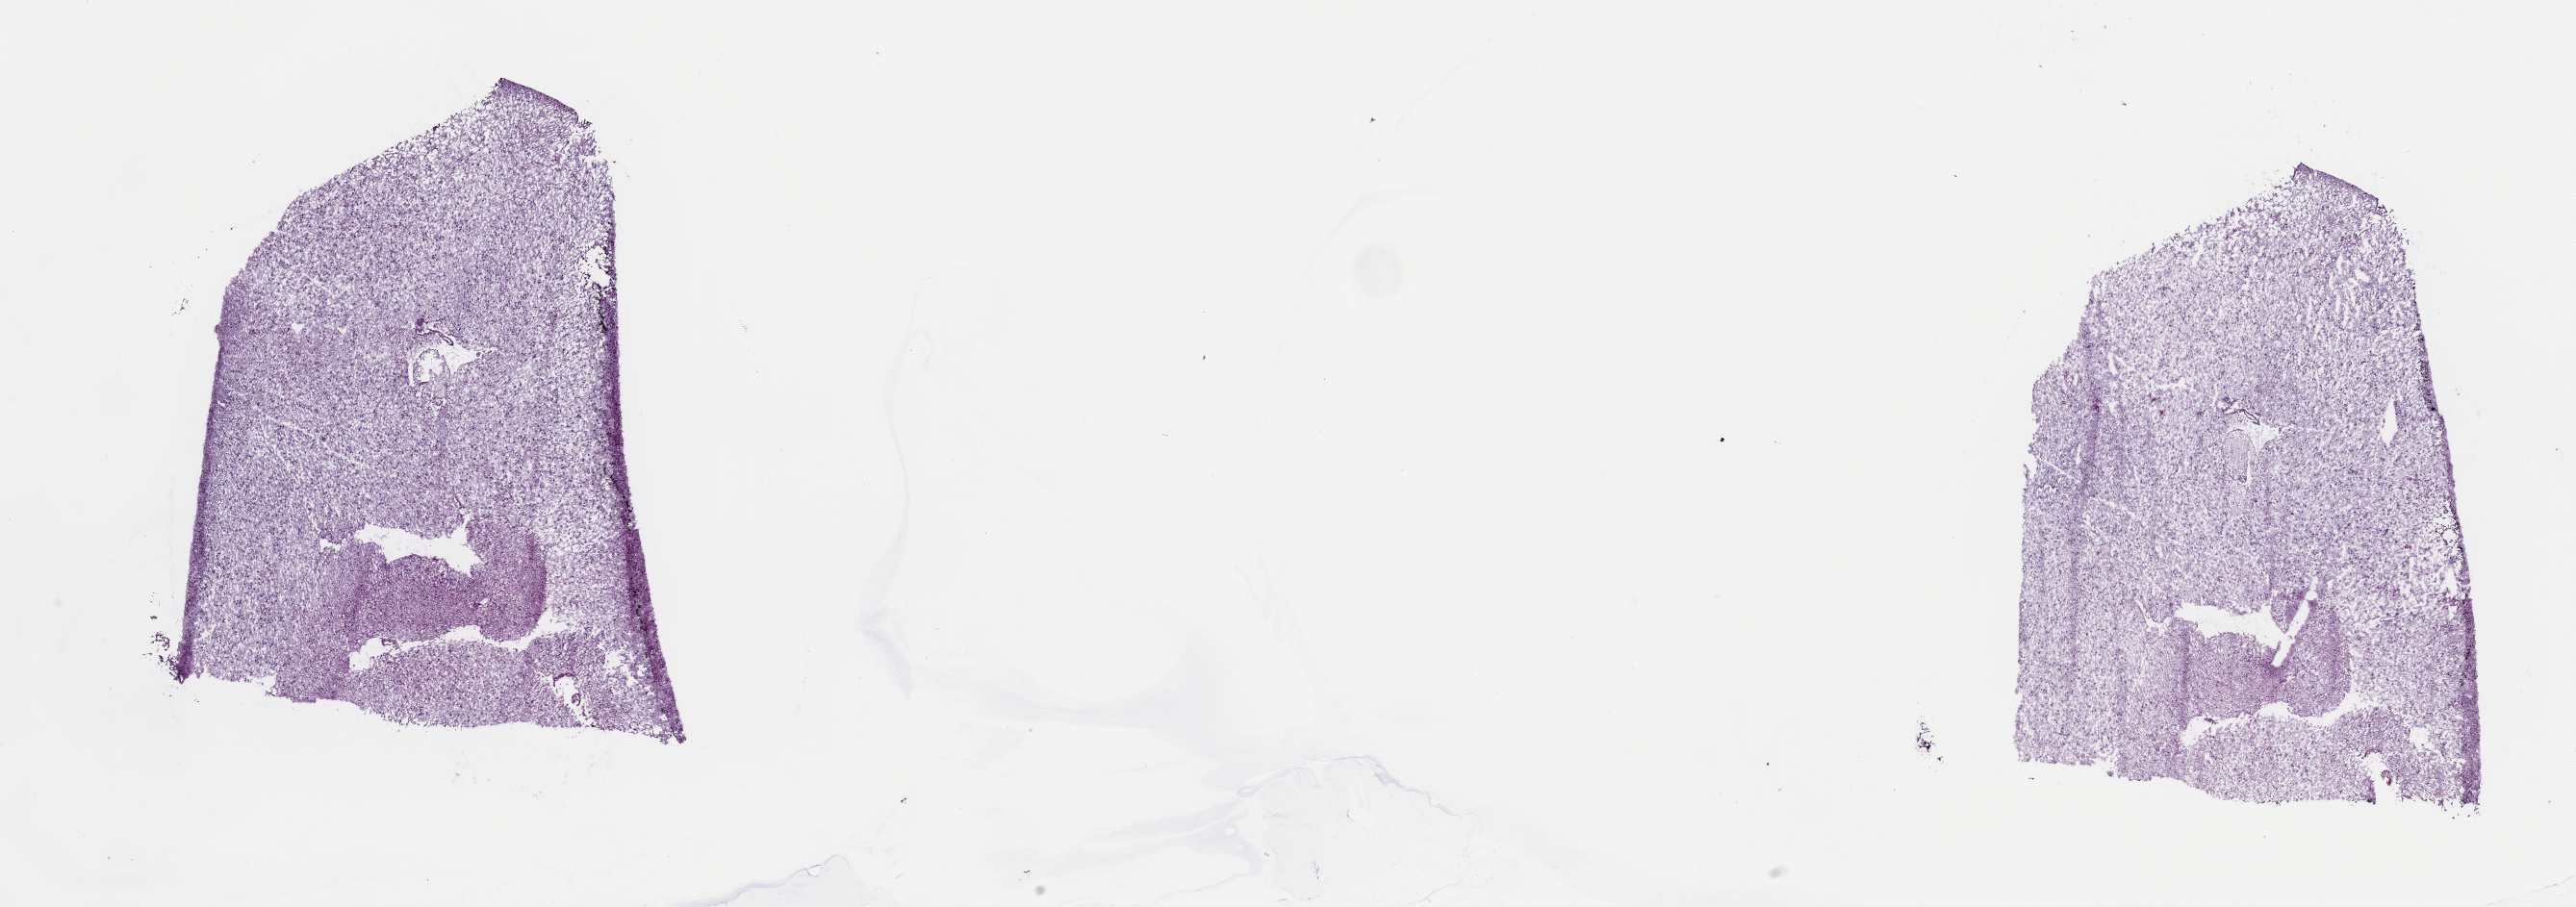
Whole-slide histology image, H&E — a low-resolution overview of the entire scanned area, about 21.1 x 7.4 mm (acquisition: 40x scan), frozen section from the top of the tissue portion, sample: primary tumour, brain. Patient: female, age at initial diagnosis 42 years.
Pathologic diagnosis: Astrocytoma, NOS (cerebrum).